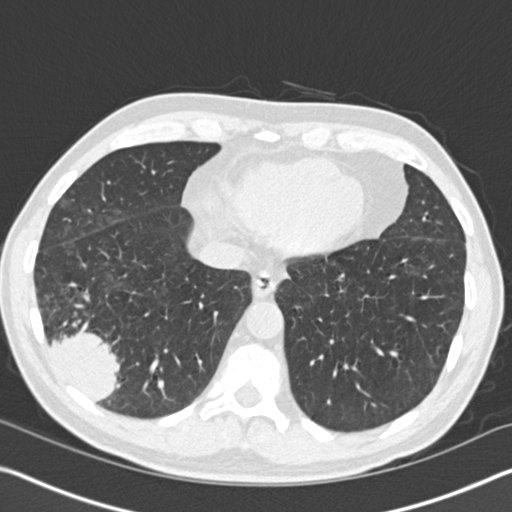
Low-dose screening chest CT, axial slice. Baseline annual screen. Lung window (W 1500 / L -600 HU). 2 mm slice thickness. Standard (soft-tissue) reconstruction kernel (B30f). Male participant, aged 61 years at enrolment. Current smoker at enrolment.
- Expert-annotated lung lesion, bounding box <21,289,143,416> (left, top, right, bottom; pixels).
- Screening reader's record for this exam (one nodule recorded; not confirmed to be the boxed lesion): non-calcified nodule or mass ≥4 mm, right lower lobe, 52 × 36 mm, spiculated (stellate) margins, soft tissue attenuation.
- Official screen result: positive, change unspecified: nodule(s) >= 4 mm or enlarging nodule(s), mass(es), or other non-specific abnormalities suspicious for lung cancer.
- Later outcome: lung cancer diagnosed 392 days after this screen — bronchiolo-alveolar adenocarcinoma, NOS, right lower lobe, moderately differentiated (G2), stage IIIB (AJCC 6th edition), 90 mm at pathology.